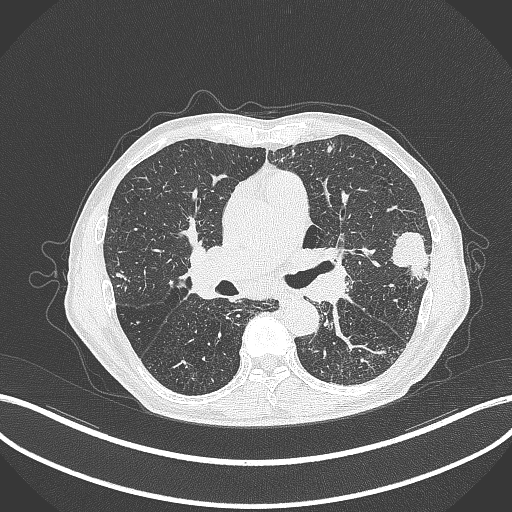
Chest CT, one axial slice. Position 234 of 463 along the scan axis. 120 kVp. Lung window (W 1500 / L -600 HU). 1 mm slice thickness. 512 × 512 image matrix, field of view 400 × 400 mm. Patient: male, 74 years. Case-level facts recorded for this patient, not image findings: clinical TNM (as recorded): T2a N1 M0.
Annotated regions visible in this slice (rectangle marked by the reading radiologist):
- lung tumour (recorded histology: adenocarcinoma): bounding box <387,228,431,288> (left, top, right, bottom; pixels)